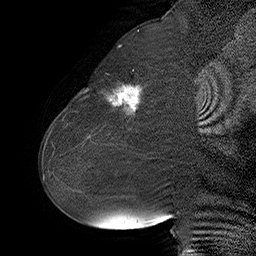
Breast MRI (dynamic contrast-enhanced), one sagittal slice. Position 25 of 55 along the scan axis. Dynamic contrast-enhanced series, time point 2 of 6 at this slice position (early post-contrast). 1.5 T. TE 4.5 ms, TR 32.4 ms. 3 mm slice thickness. 256 × 256 image matrix. Female patient. Case-level facts recorded for this patient, not image findings: setting: breast cancer imaged before/during neoadjuvant chemotherapy; receptor status: HER2-positive.
Structures marked on this image (semi-automatic segmentation, software-assisted and operator-edited):
- analysis volume of interest (the breast-tissue region the enhancement analysis was run in; not a lesion): bounding box <80,64,163,134> (left, top, right, bottom; pixels)
- tumour enhancement mask (voxels above the 100 % enhancement threshold inside the analysis volume of interest): <85,85,141,115>